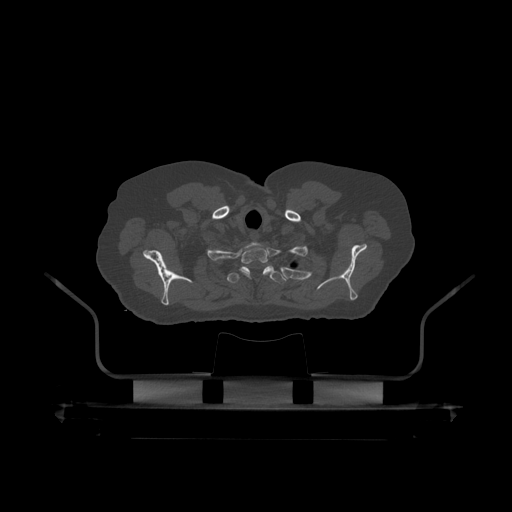
CT including the spine, one axial slice. Reconstruction kernel STANDARD. Bone window (W 1800 / L 400 HU). 512 × 512 image matrix, field of view 650 × 650 mm. Patient: male, 60 years. Case-level facts recorded for this patient, not image findings: primary cancer: prostate.
Annotated regions visible in this slice (semi-automatic segmentation, software-assisted and operator-edited):
- T1 vertebra: bounding box <240,243,271,277> (left, top, right, bottom; pixels)
- T2 vertebra: <227,266,287,285>